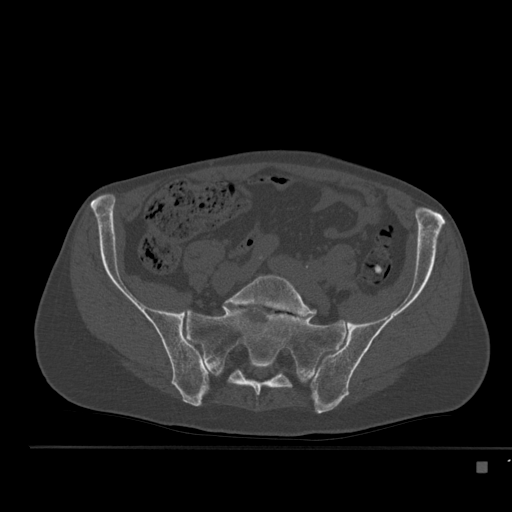
CT including the spine, one axial slice; slice 108 of 517 in the series (ordered by position); reconstruction kernel Br40s; 120 kVp; bone window (W 1800 / L 400 HU); 1.5 mm slice thickness; 512 × 512 image matrix, field of view 408 × 408 mm. Patient: male, 70 years. Case-level facts recorded for this patient, not image findings: primary cancer: renal; vertebrae with lytic lesions (as recorded): T4, T6, T10, T12, L3, L4, L5.
Outlined on this slice (semi-automatically segmented with operator editing):
- L5 vertebra: bounding box <224,274,315,318> (left, top, right, bottom; pixels)